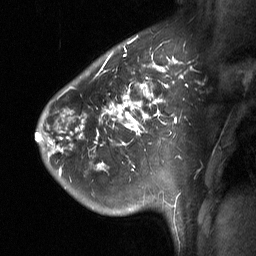
Breast MRI (dynamic contrast-enhanced), one sagittal slice; position 49 of 64 along the scan axis; dynamic contrast-enhanced study with each time point stored as its own series, time point 2 of 3 at this slice position (early post-contrast, ordered by acquisition time); 1.5 T; TE 4.8 ms, TR 27 ms; 256 × 256 image matrix, field of view 200 × 200 mm. Patient: female, 42 years. Case-level facts recorded for this patient, not image findings: setting: breast cancer imaged before/during neoadjuvant chemotherapy; receptor status: triple-negative.
Outlined on this slice (semi-automatically segmented with operator editing):
- analysis volume of interest (the breast-tissue region the enhancement analysis was run in; not a lesion): bounding box [x1, y1, x2, y2] px = [49, 45, 198, 197]
- tumour enhancement mask (voxels above the 90 % enhancement threshold inside the analysis volume of interest): [50, 54, 177, 169]